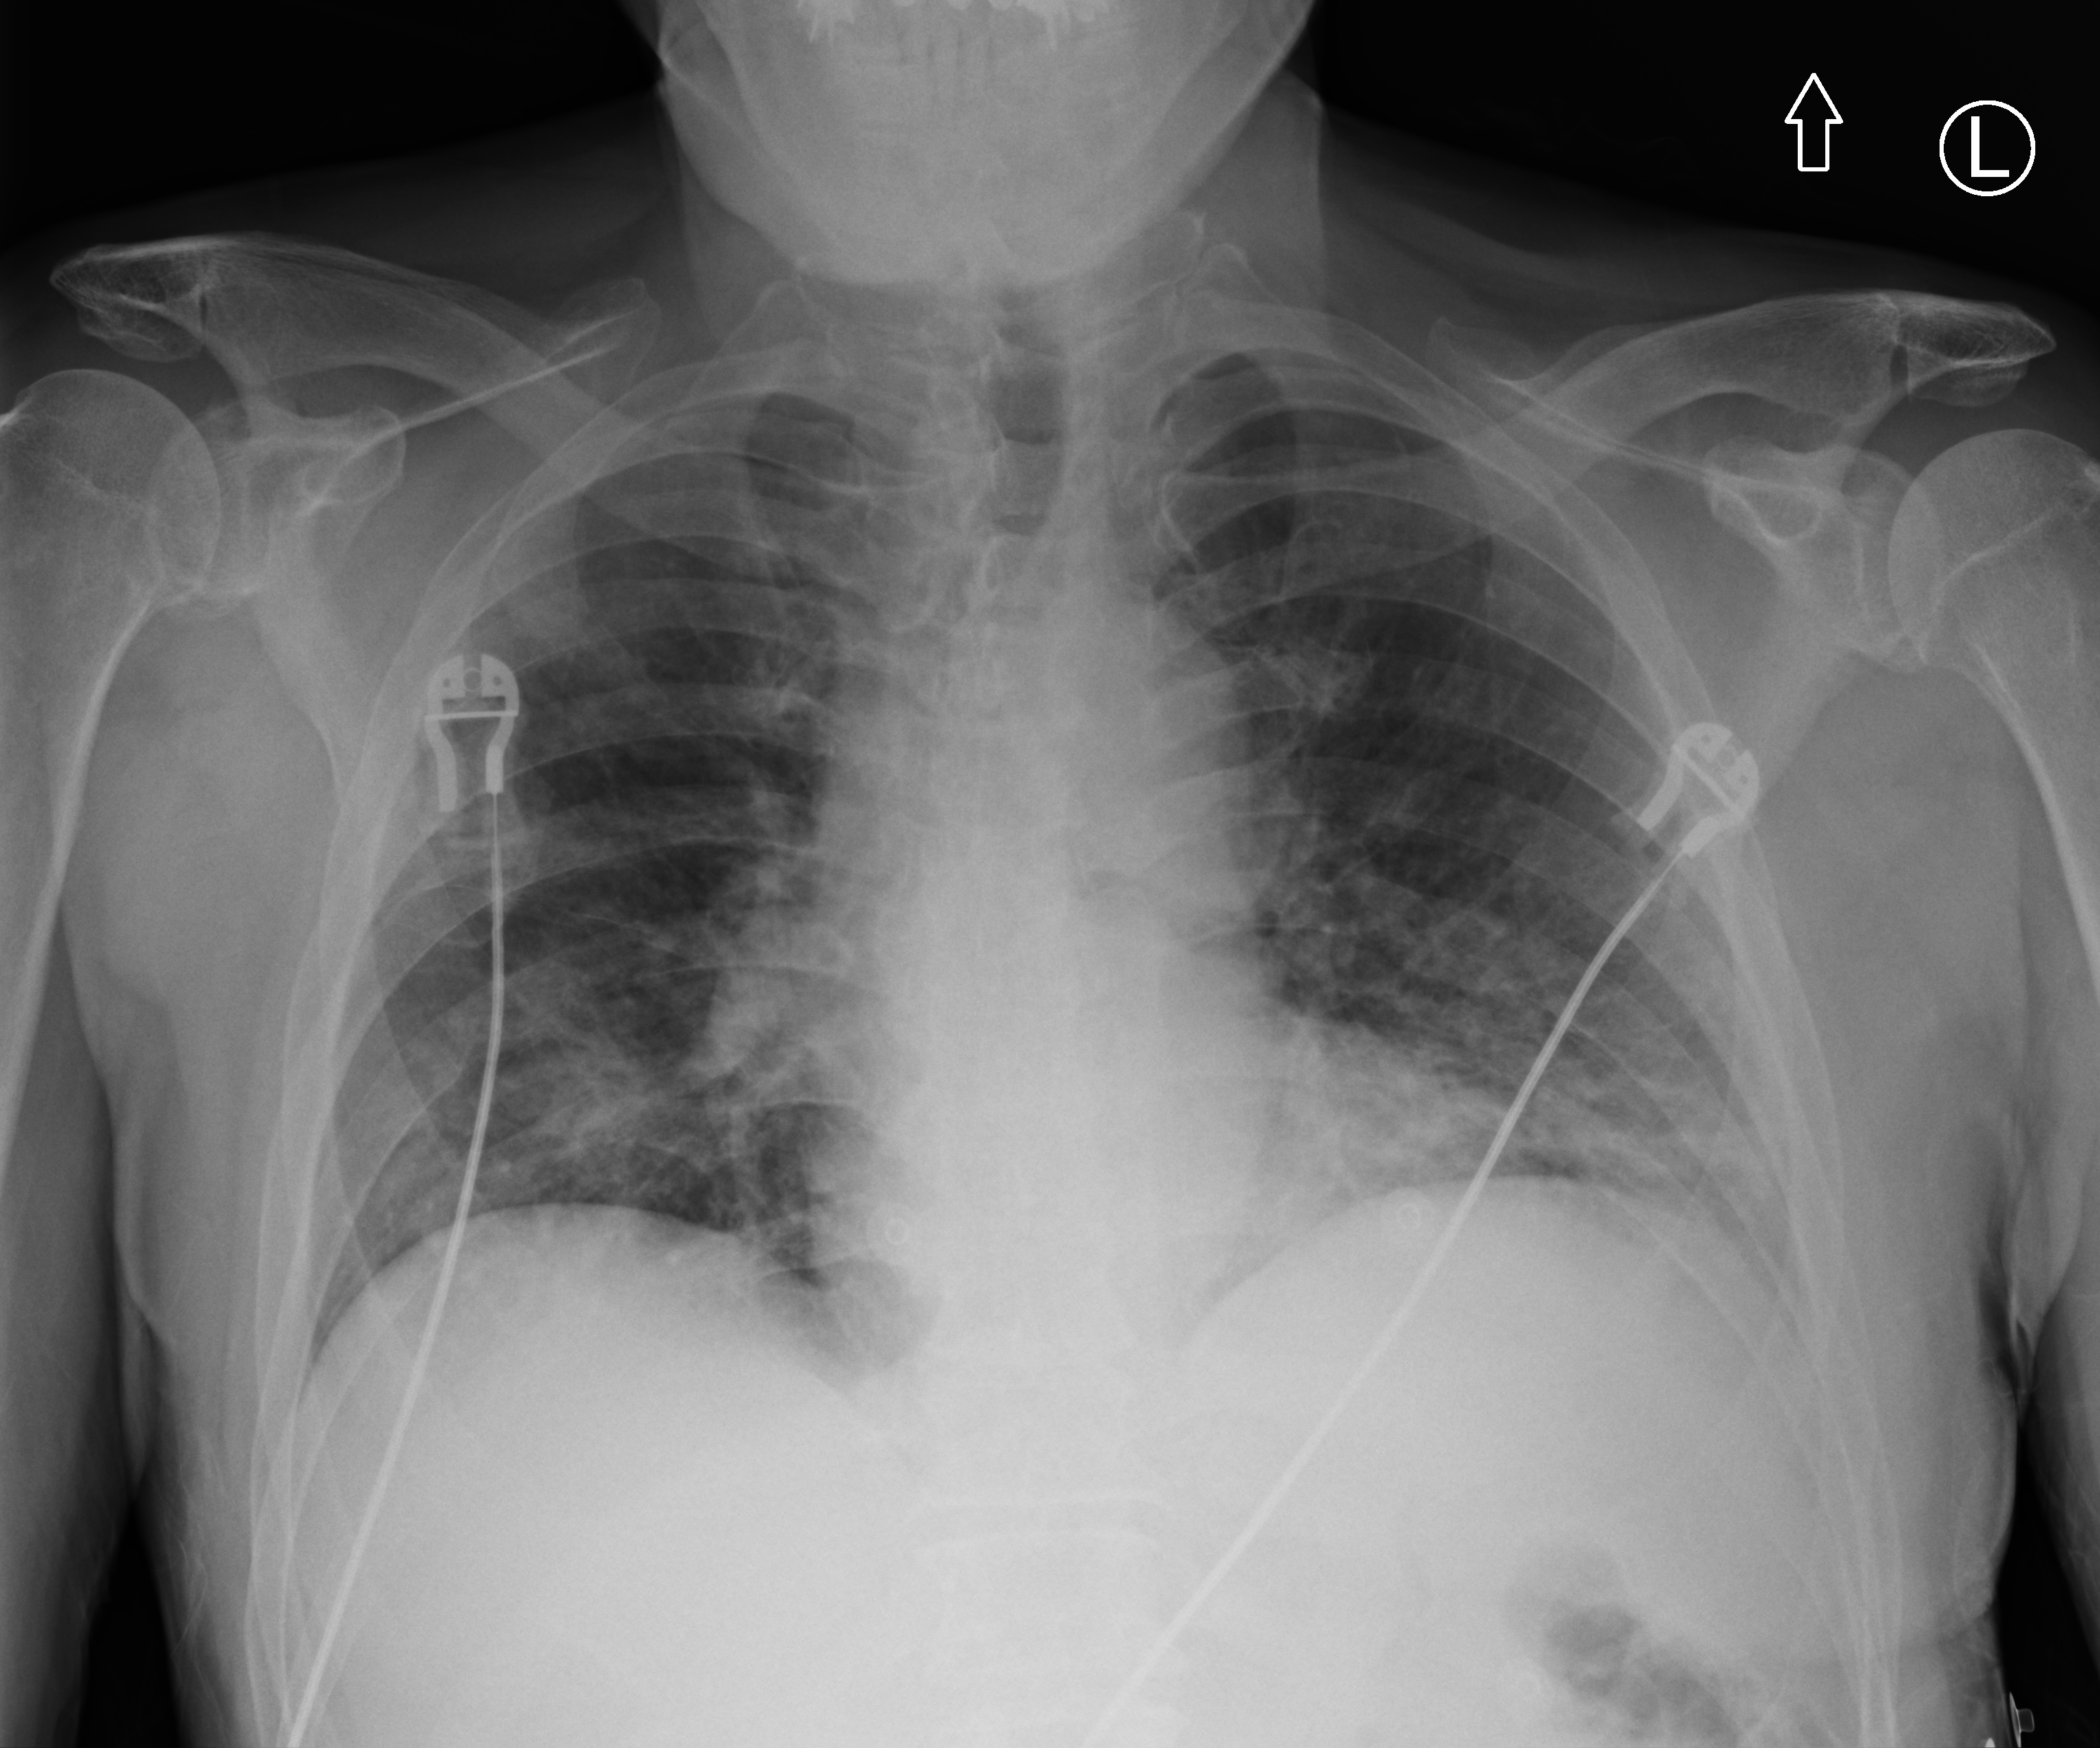
Chest X-ray (portable); anteroposterior (AP) projection. Male patient hospitalised with COVID-19, age 60–74 years.
Admission-level facts for this patient (not findings on this image; timing relative to this image not recorded): COPD (admission record): no; other chronic lung disease (admission record): no.